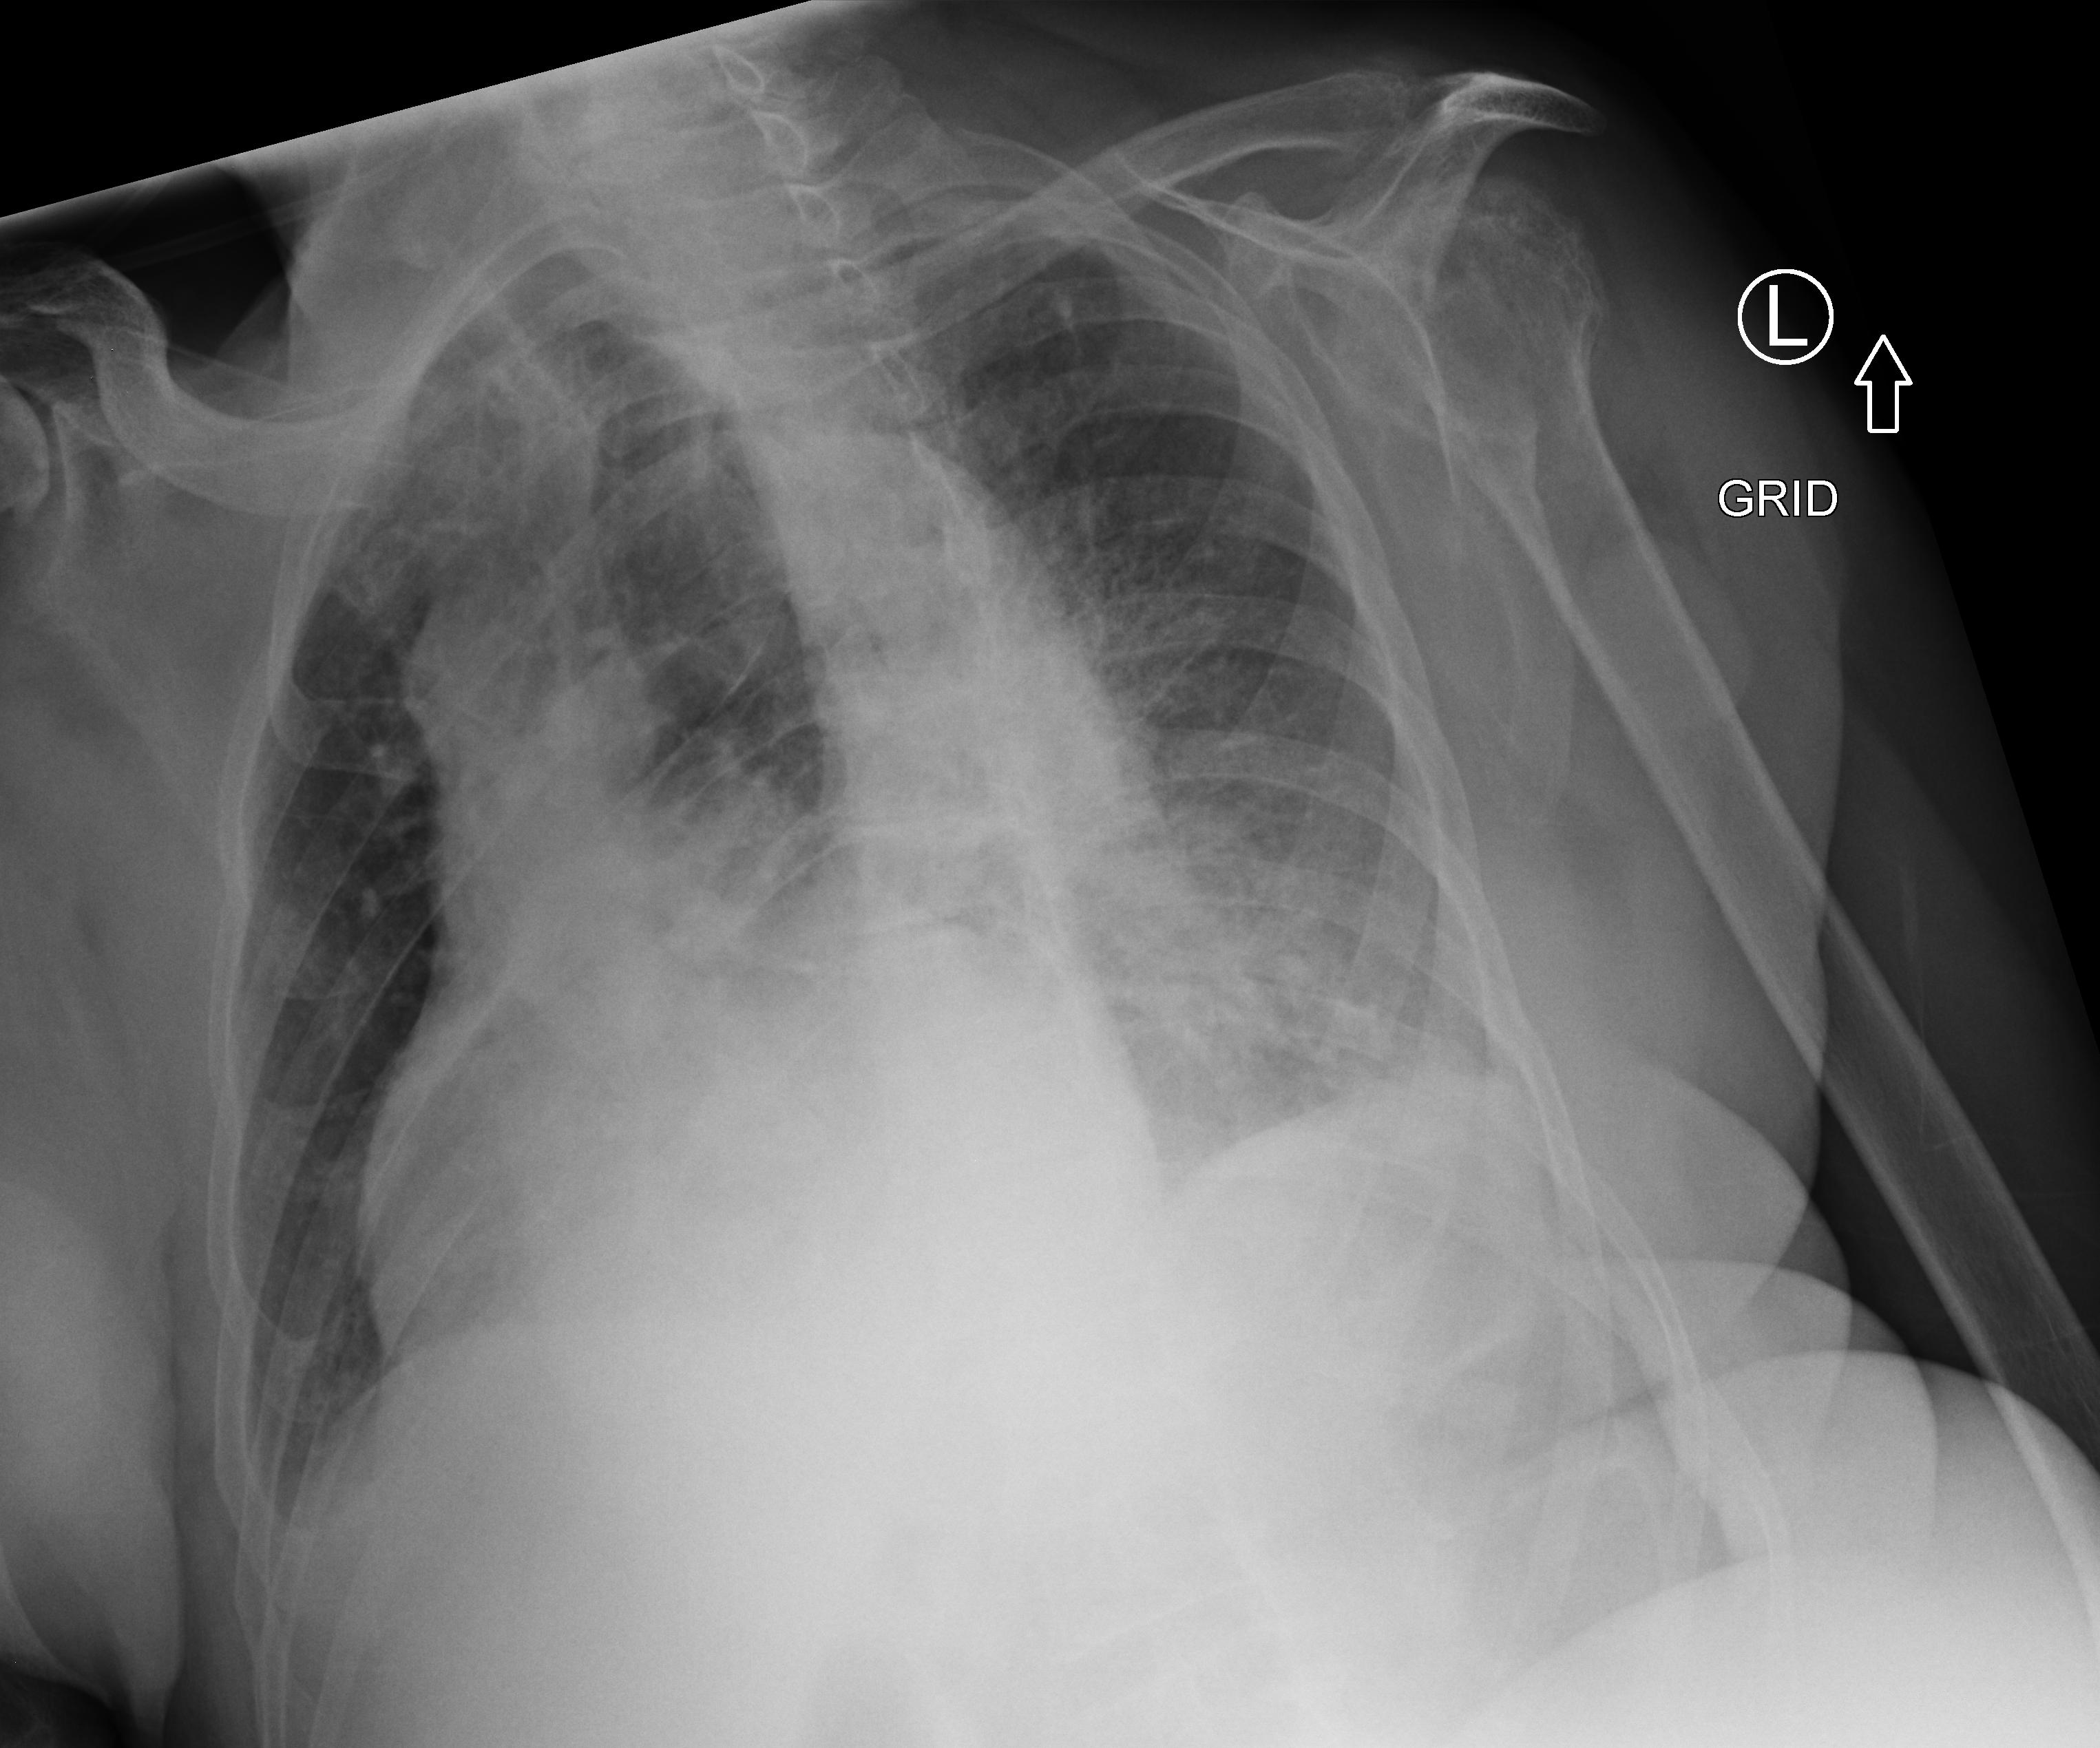
Chest X-ray (portable); anteroposterior (AP) projection. Patient hospitalised with COVID-19; male, aged 75–90 years.
Hospital-stay facts (about this admission, not read from this image; timing relative to this image not recorded):
- mechanically ventilated during this hospital stay: no
- diabetes (admission record): no
- other chronic lung disease (admission record): no